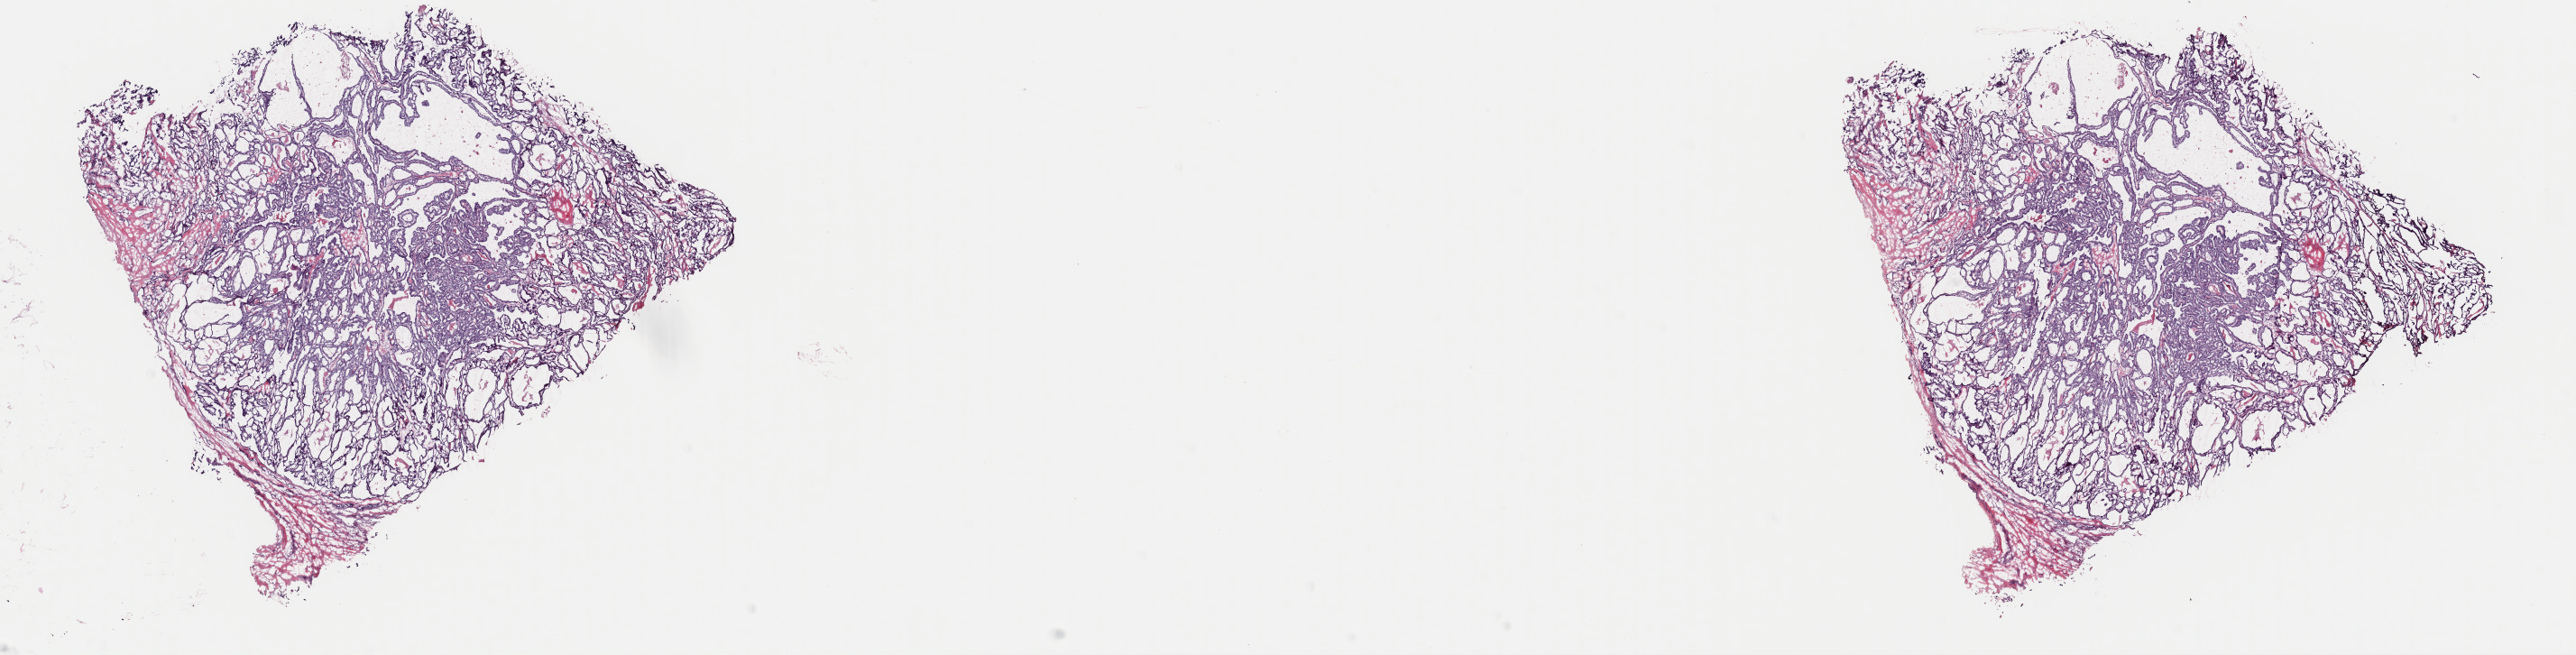
Whole-slide histology image, H&E-stained, shown as a low-resolution overview of the whole scanned area (about 22.6 x 5.7 mm); frozen section from the top of the tissue portion; primary tumour sample from the thyroid. Patient: female, age at initial diagnosis 31 years. Pathologist review of this section (percent, as recorded): tumour cells 80%, tumour nuclei 100%, normal cells 0%, stromal cells 20%, necrosis 0%. Inflammatory infiltration, as recorded: lymphocyte infiltration 0%, monocyte infiltration 1%, neutrophil infiltration 0%.
TNM: T3 N1 M0. AJCC pathologic stage: I (7th edition). Histologic diagnosis: Papillary adenocarcinoma, NOS (thyroid gland). Lymph nodes positive (case pathology): 1 of 4 examined.